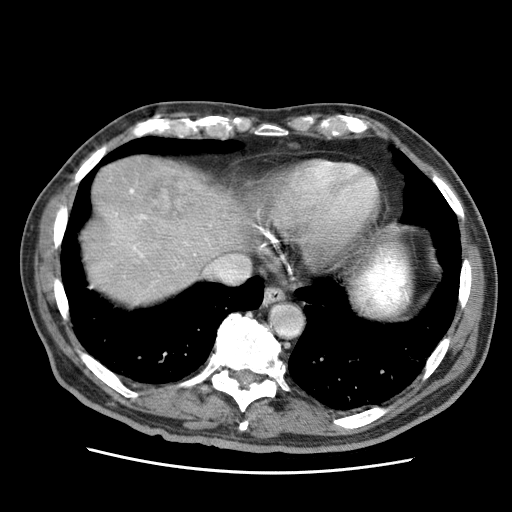
Contrast-enhanced abdominal CT (liver protocol), one axial slice. Position 59 of 75 along the scan axis. Reconstruction kernel STANDARD. Soft-tissue window (W 400 / L 40 HU). 2.5 mm slice thickness. 512 × 512 image matrix. From the clinical record (not read from this slice): diagnosis: hepatocellular carcinoma (patient treated with transarterial chemoembolisation; whether this scan precedes or follows treatment is not stated here); TNM stage (as recorded): Stage-IIIA; Child-Pugh class: A; tumour differentiation: well differentiated.
Annotated regions visible in this slice (semi-automatically segmented with operator editing):
- liver parenchyma outside the tumour (the mass and vessels are separate outlines, so this box may not span the whole liver): bounding box <82,156,250,304> (left, top, right, bottom; pixels)
- mass: <143,176,192,232>
- liver vessels: <115,189,208,258>